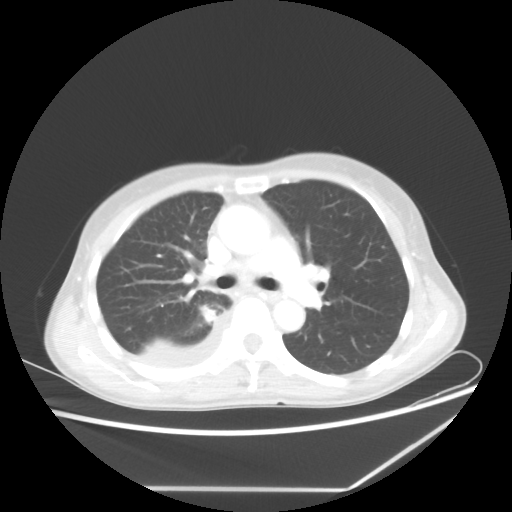
Chest CT, one axial slice; position 37 of 60 along the scan axis; lung window (W 1500 / L -600 HU); 5 mm slice thickness; 512 × 512 image matrix. Patient: female, 59 years. From the clinical record (not read from this slice): clinical TNM (as recorded): T1c N1 M1.
Outlined on this slice (bounding box drawn by a radiologist):
- lung tumour (recorded histology: adenocarcinoma): box from (x=201, y=306) to (x=219, y=324) px